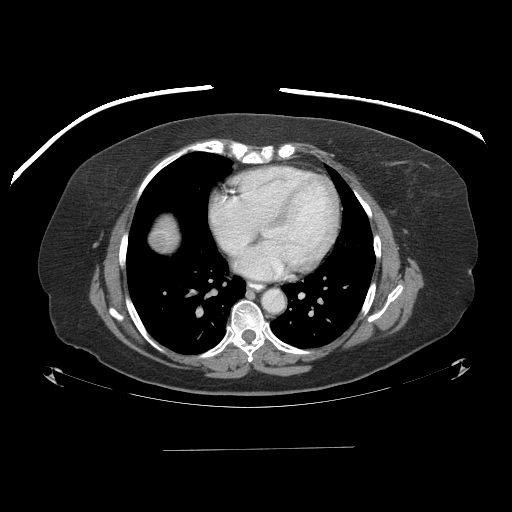
Contrast-enhanced abdominal CT (liver protocol), one axial slice; position 90 of 103 along the scan axis; reconstruction kernel STANDARD; one of 2 acquisitions stored at this slice position; soft-tissue window (W 400 / L 40 HU); 2.5 mm slice thickness; 512 × 512 image matrix, field of view 500 × 500 mm. Case-level facts recorded for this patient, not image findings: diagnosis: hepatocellular carcinoma (patient treated with transarterial chemoembolisation; whether this scan precedes or follows treatment is not stated here); TNM stage (as recorded): Stage-IIIA; Child-Pugh class: A; tumour size: 5.2 cm.
Outlined on this slice (semi-automatically segmented with operator editing):
- liver parenchyma outside the tumour (the mass and vessels are separate outlines, so this box may not span the whole liver): bounding box [x1, y1, x2, y2] px = [150, 216, 176, 250]